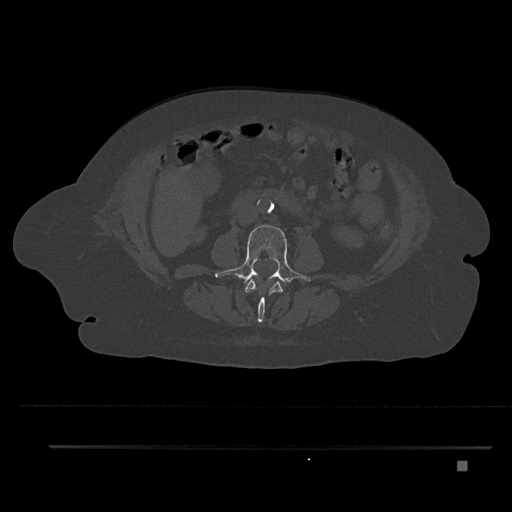
CT including the spine, one axial slice. Slice 137 of 797 in the series (ordered by position). 120 kVp. Bone window (W 1800 / L 400 HU). 0.5 mm slice thickness. 512 × 512 image matrix, field of view 437 × 437 mm. Patient: female, 76 years. Case-level facts recorded for this patient, not image findings: primary cancer: lung; vertebrae with lytic lesions (as recorded): T11, L3.
Outlined on this slice (semi-automatically segmented with operator editing):
- L2 vertebra: bounding box (x1, y1, x2, y2) in pixels: (245, 280, 283, 323)
- L3 vertebra: (215, 225, 311, 288)